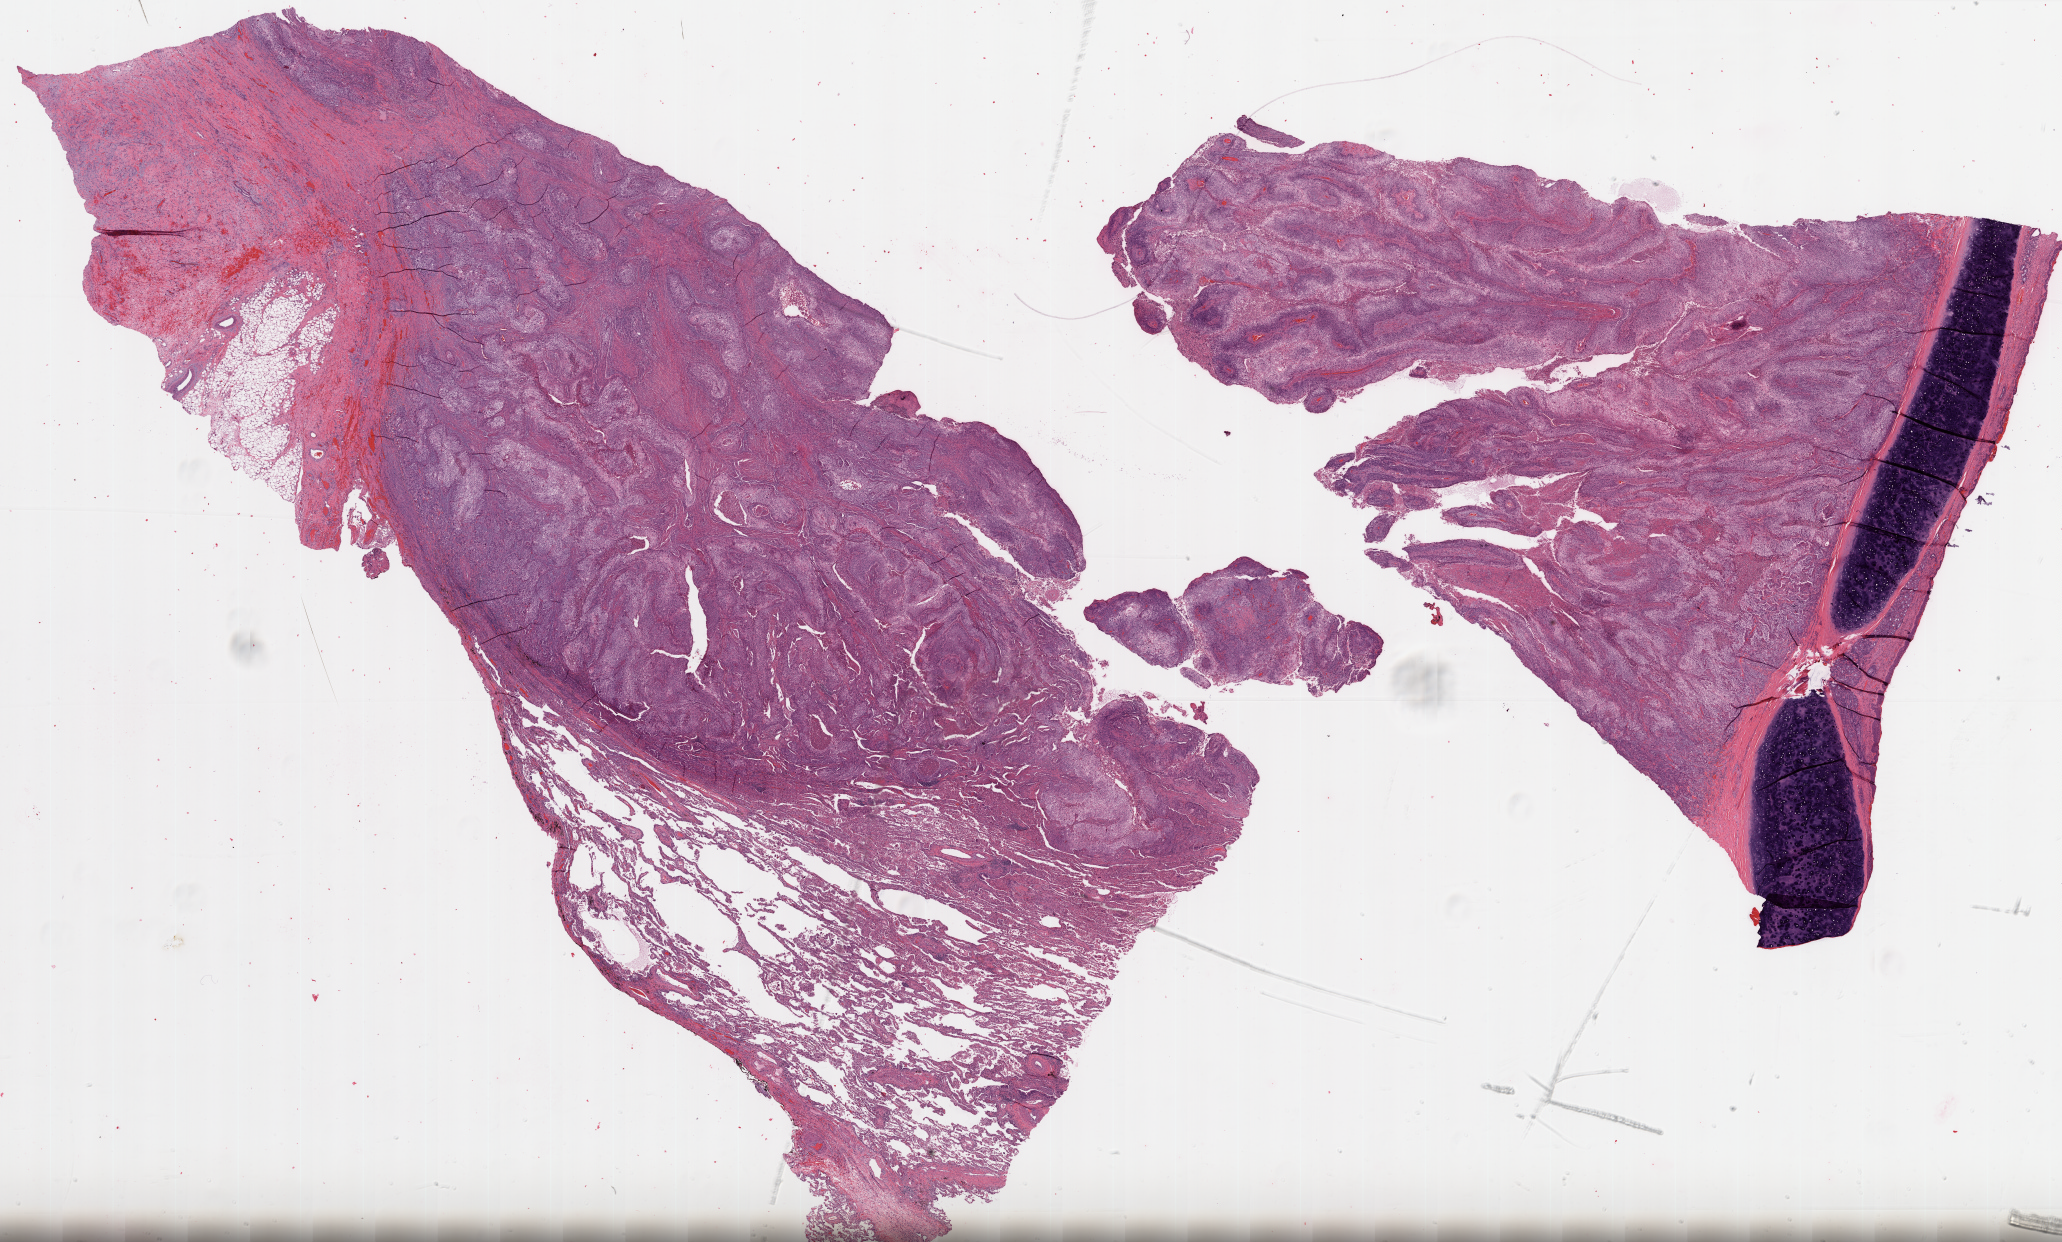
H&E whole-slide image, whole scanned area (about 33.1 x 20.0 mm, from a 20x scan) shown as a low-resolution overview, formalin-fixed paraffin-embedded (FFPE) diagnostic section, lung, primary tumour sample. Patient: male, age at initial diagnosis 47 years.
• pathologic diagnosis: Squamous cell carcinoma, NOS
• AJCC pathologic stage: IIIA
• TNM: T3 N1 M0